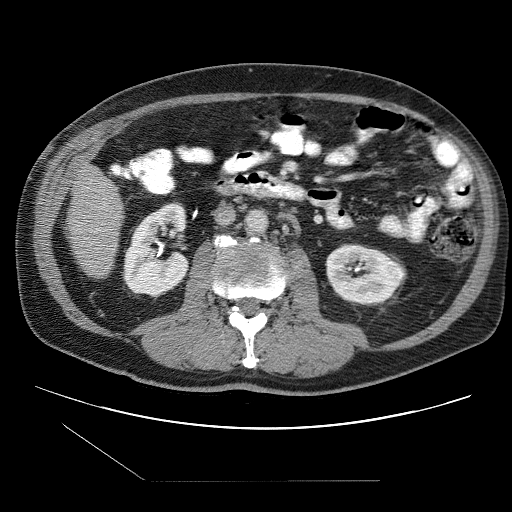
Contrast-enhanced abdominal CT (liver protocol), one axial slice. Reconstruction kernel STANDARD. 120 kVp. One of 2 acquisitions stored at this slice position. Soft-tissue window (W 400 / L 40 HU). 2.5 mm slice thickness. 512 × 512 image matrix. From the clinical record (not read from this slice): diagnosis: hepatocellular carcinoma (patient treated with transarterial chemoembolisation; whether this scan precedes or follows treatment is not stated here); TNM stage (as recorded): Stage-IIIB; Child-Pugh class: A; tumour nodularity: multinodular.
Outlined on this slice (semi-automatically segmented with operator editing):
- liver parenchyma outside the tumour (the mass and vessels are separate outlines, so this box may not span the whole liver): bounding box [x1, y1, x2, y2] px = [66, 170, 124, 276]
- liver vessels: [96, 227, 111, 247]